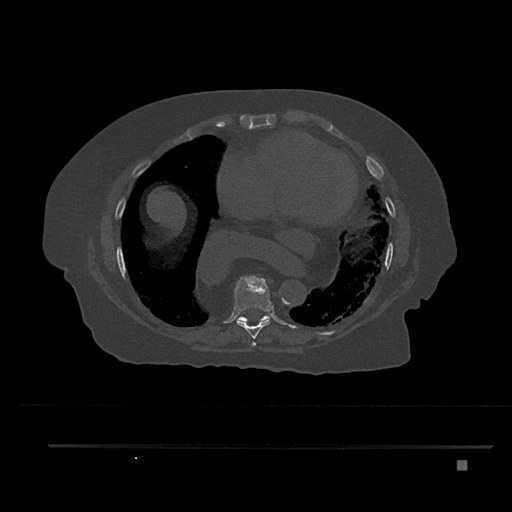
CT including the spine, one axial slice; reconstruction kernel Br40s/3; 120 kVp; bone window (W 1800 / L 400 HU); 0.5 mm slice thickness; 512 × 512 image matrix. Female patient, age 76 years. From the clinical record (not read from this slice): primary cancer: lung; vertebrae with lytic lesions (as recorded): T11, L3.
Structures marked on this image (semi-automatic segmentation, software-assisted and operator-edited):
- T7 vertebra: bounding box [x1, y1, x2, y2] px = [252, 342, 256, 345]
- T8 vertebra: [234, 276, 271, 347]
- T9 vertebra: [237, 315, 270, 322]